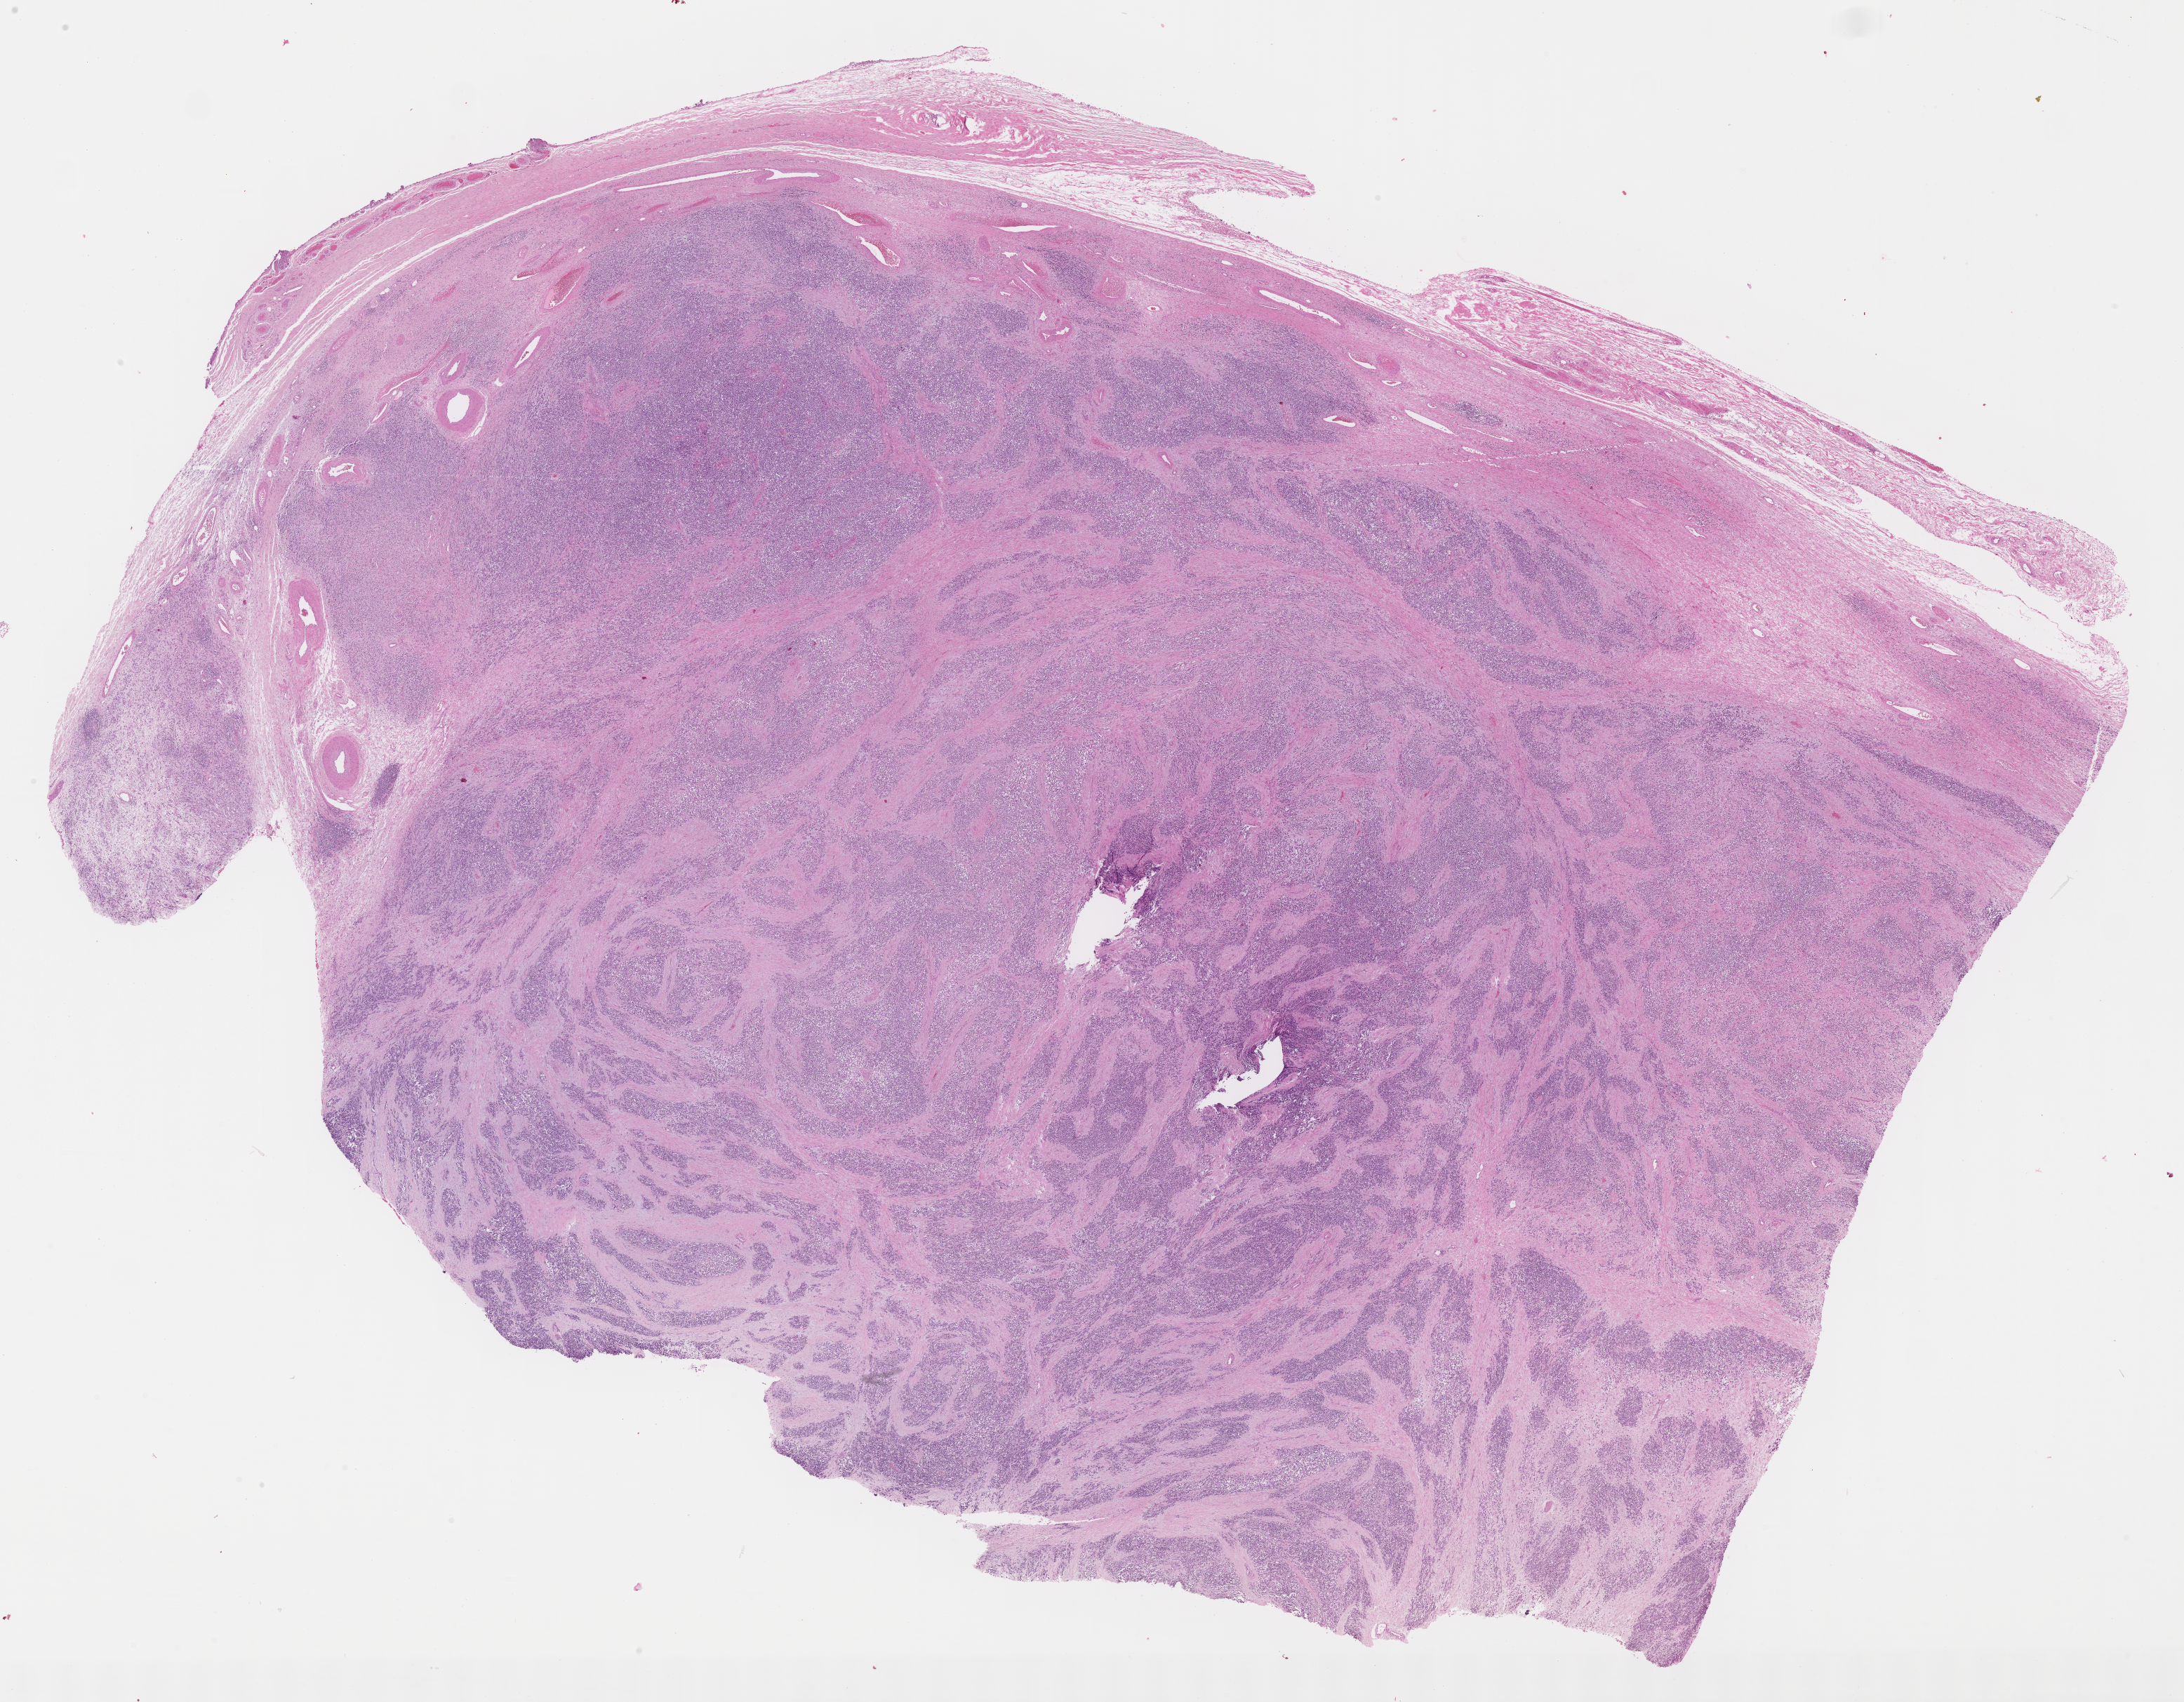
Digitized hematoxylin and eosin (H&E)-stained section of tumor tissue — low-resolution overview of the scanned area, about 25.2 x 19.6 mm. FFPE section. Sample anatomic site: testicle, right. Patient: male, age 16.6 years at diagnosis.
Diagnosis: rhabdomyosarcoma; histological classification: embryonal rhabdomyosarcoma. Primary site (case record): testis-paratesticular. Stage (as recorded): 1. Metastatic status at presentation (as recorded): non-metastatic (confirmed).